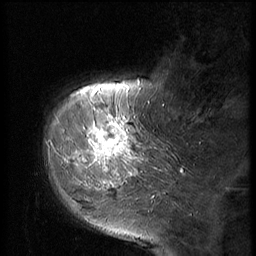
Breast MRI (dynamic contrast-enhanced), one sagittal slice; position 13 of 56 along the scan axis; dynamic contrast-enhanced series, image 2 of 2 at this slice position (ordered by acquisition); 1.5 T; TE 4.2 ms, TR 9 ms; 256 × 256 image matrix, field of view 180 × 180 mm. Female patient, age 51 years. Case-level facts recorded for this patient, not image findings: setting: breast cancer imaged before/during neoadjuvant chemotherapy; receptor status: triple-negative.
Outlined on this slice (semi-automatic segmentation, software-assisted and operator-edited):
- analysis volume of interest (the breast-tissue region the enhancement analysis was run in; not a lesion): bounding box <60,98,147,197> (left, top, right, bottom; pixels)
- tumour enhancement mask (voxels above the 140 % enhancement threshold inside the analysis volume of interest): <76,116,135,175>